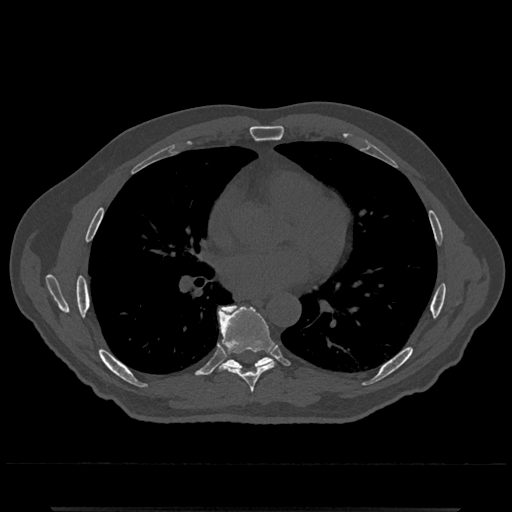
CT including the spine, one axial slice; 120 kVp; bone window (W 1800 / L 400 HU); 0.5 mm slice thickness; 512 × 512 image matrix, field of view 393 × 393 mm. Patient: male, 67 years. Case-level facts recorded for this patient, not image findings: primary cancer: prostate.
Annotated regions visible in this slice (semi-automatic segmentation, software-assisted and operator-edited):
- T7 vertebra: bounding box [x1, y1, x2, y2] px = [219, 307, 276, 393]
- T8 vertebra: [219, 305, 272, 370]